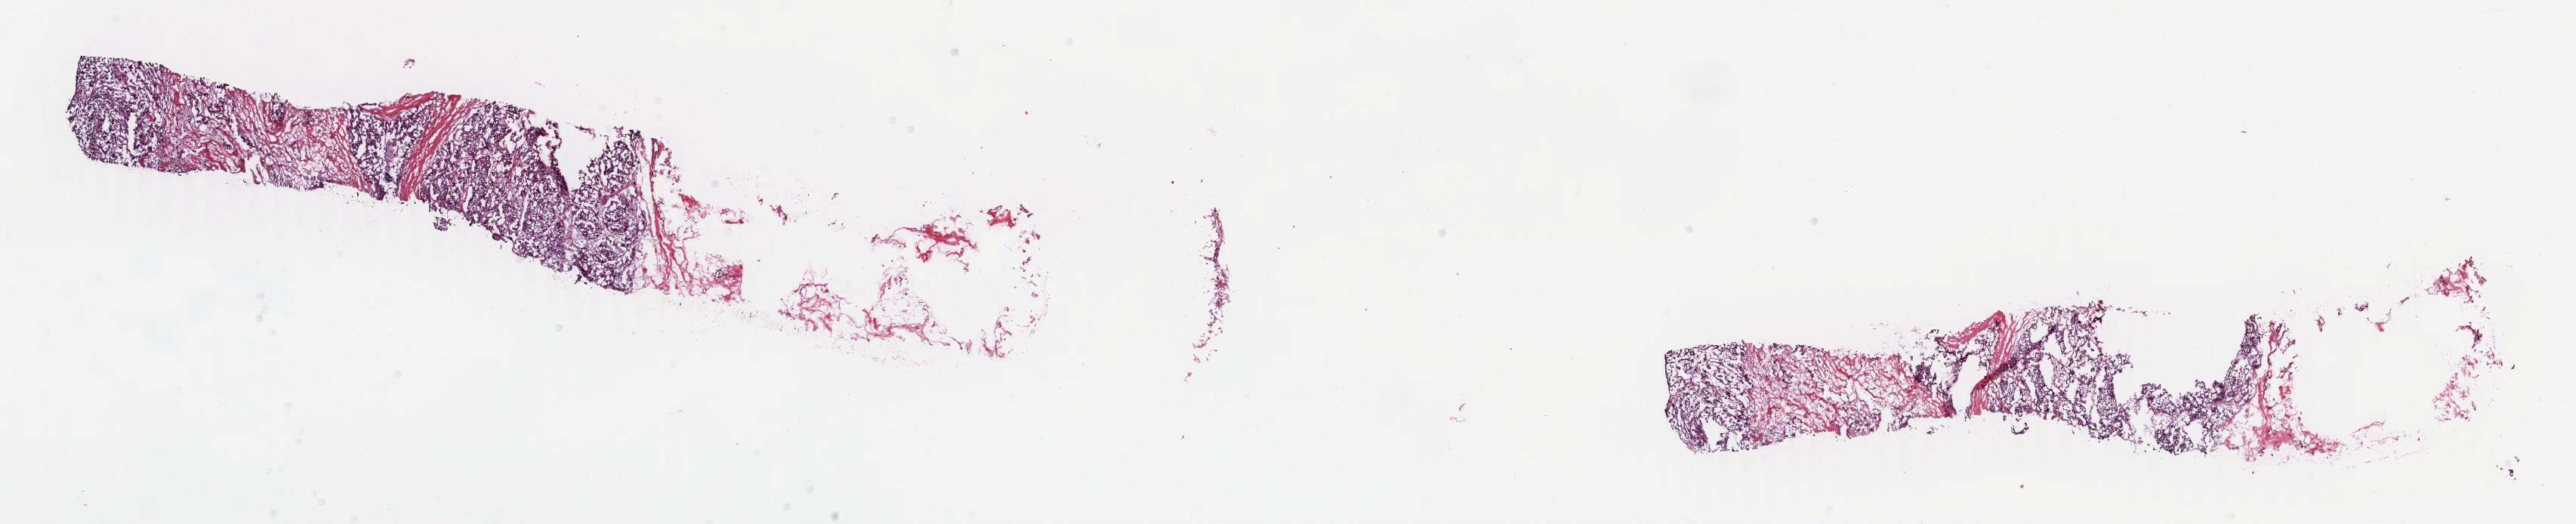
Digitized Hematoxylin and eosin (H&E) stained tissue section (whole slide) — a low-resolution overview of the entire scanned area, about 27.1 x 5.5 mm, frozen section, breast, primary tumour sample. Patient: female, age at initial diagnosis 51 years. Pathologist review of this section (percent, as recorded): tumour cells 65%, tumour nuclei 85%.
Diagnosis: Infiltrating duct carcinoma, NOS.